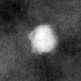
Cropped region of a digitized screen-film mammogram centred on a radiologist-marked abnormality; left breast; CC view; BI-RADS breast density category 2 (scale 1–4).
Finding: calcifications, morphology coarse / round and regular / lucent center; BI-RADS assessment category 2; benign; no additional work-up was recommended (benign without callback).